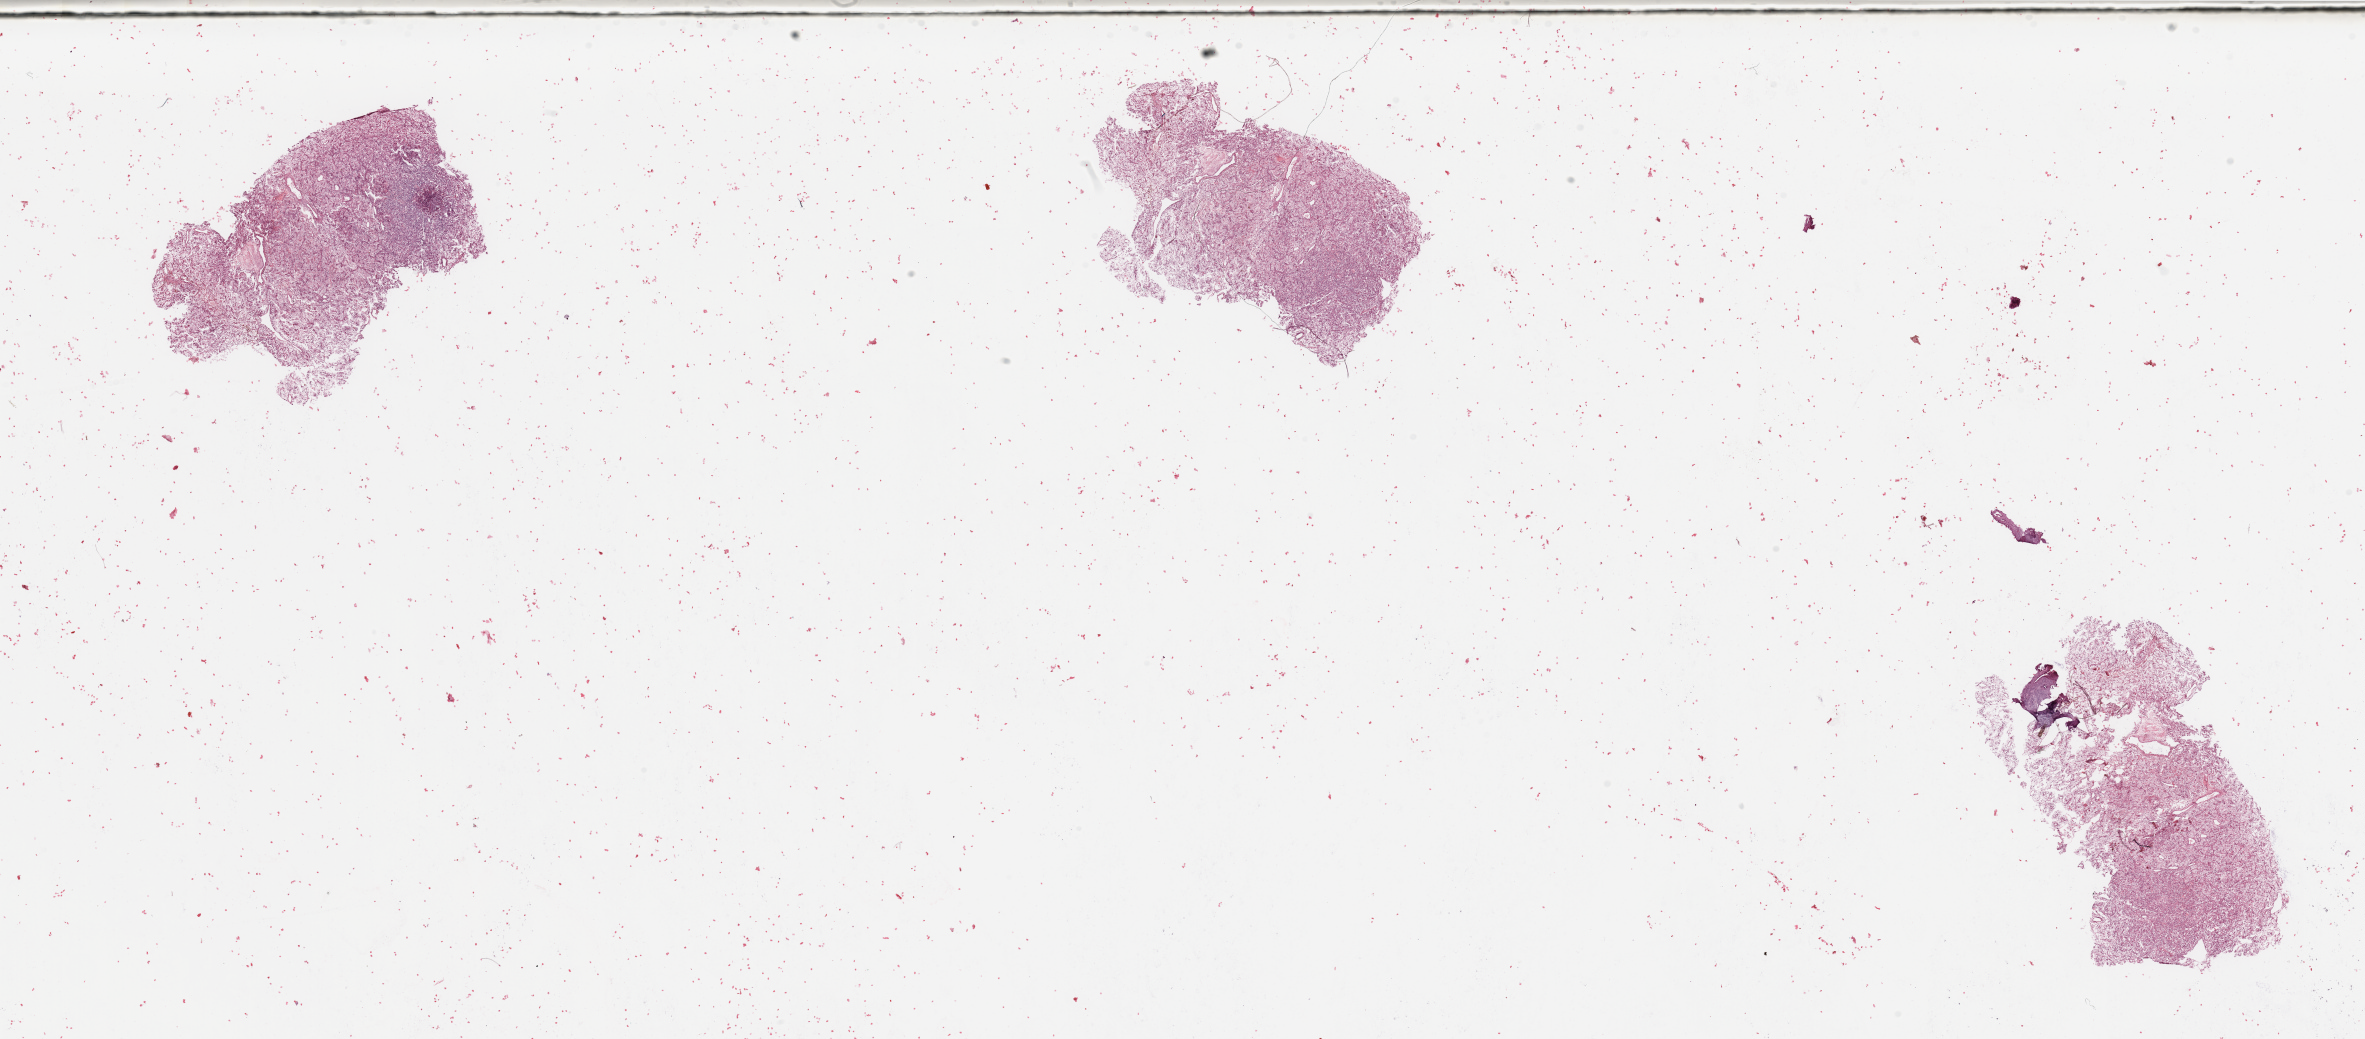
Whole-slide histology image, H&E-stained, a low-resolution overview of the entire scanned area, about 37.4 x 16.4 mm (from a 20x scan), tumour tissue sample, sampled site: kidney. Male, 67 y/o. Histologic grade: G3 (poorly differentiated). Pathologist review of this section (percent, as recorded): tumour nuclei 80%, necrosis 5%.
AJCC pathologic stage: I. Primary tumour site (as recorded): middle. Diagnosis: Renal cell carcinoma, NOS.